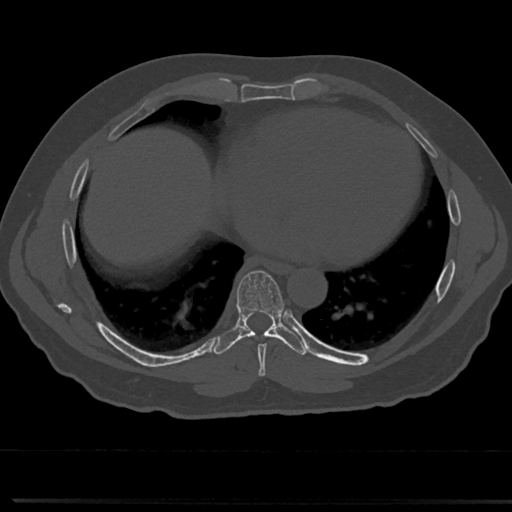
CT including the spine, one axial slice. Position 367 of 817 along the scan axis. Bone window (W 1800 / L 400 HU). 0.5 mm slice thickness. 512 × 512 image matrix, field of view 355 × 355 mm. Patient: male, 61 years. Case-level facts recorded for this patient, not image findings: primary cancer: prostate.
Annotated regions visible in this slice (semi-automatic segmentation, software-assisted and operator-edited):
- T7 vertebra: bounding box <236,272,287,358> (left, top, right, bottom; pixels)
- T8 vertebra: <237,323,283,335>